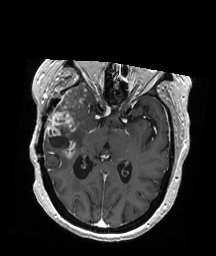
Brain MRI from a brain-tumour surgery series, one axial slice; slice 109 of 192 in the series (ordered by position); T1-weighted post-contrast; 216 × 256 image matrix. From the clinical record (not read from this slice): histopathology: Glioblastoma; WHO grade: 4; IDH mutation: no; tumour location: Right Temporal.
Annotated regions visible in this slice (expert manual segmentation):
- tumour: bounding box (x1, y1, x2, y2) in pixels: (45, 86, 86, 159)